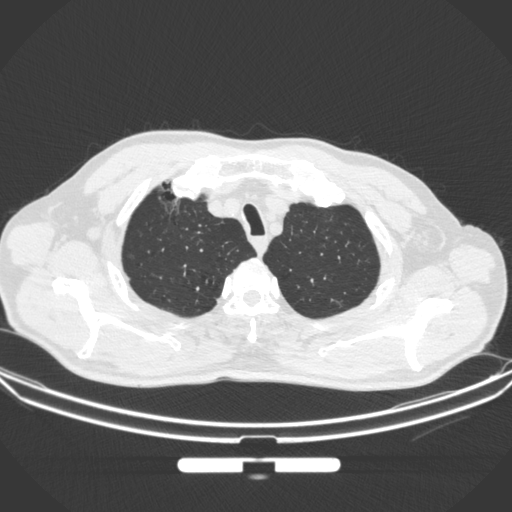
Chest CT, one axial slice. Position 298 of 355 along the scan axis. 120 kVp. Lung window (W 1500 / L -600 HU). 1 mm slice thickness. 512 × 512 image matrix. Male patient, age 67 years. From the clinical record (not read from this slice): clinical TNM (as recorded): T1c N0 M0; histopathological grade: G2.
Structures marked on this image (rectangle marked by the reading radiologist):
- lung tumour (recorded histology: adenocarcinoma): bounding box [x1, y1, x2, y2] px = [149, 183, 192, 219]